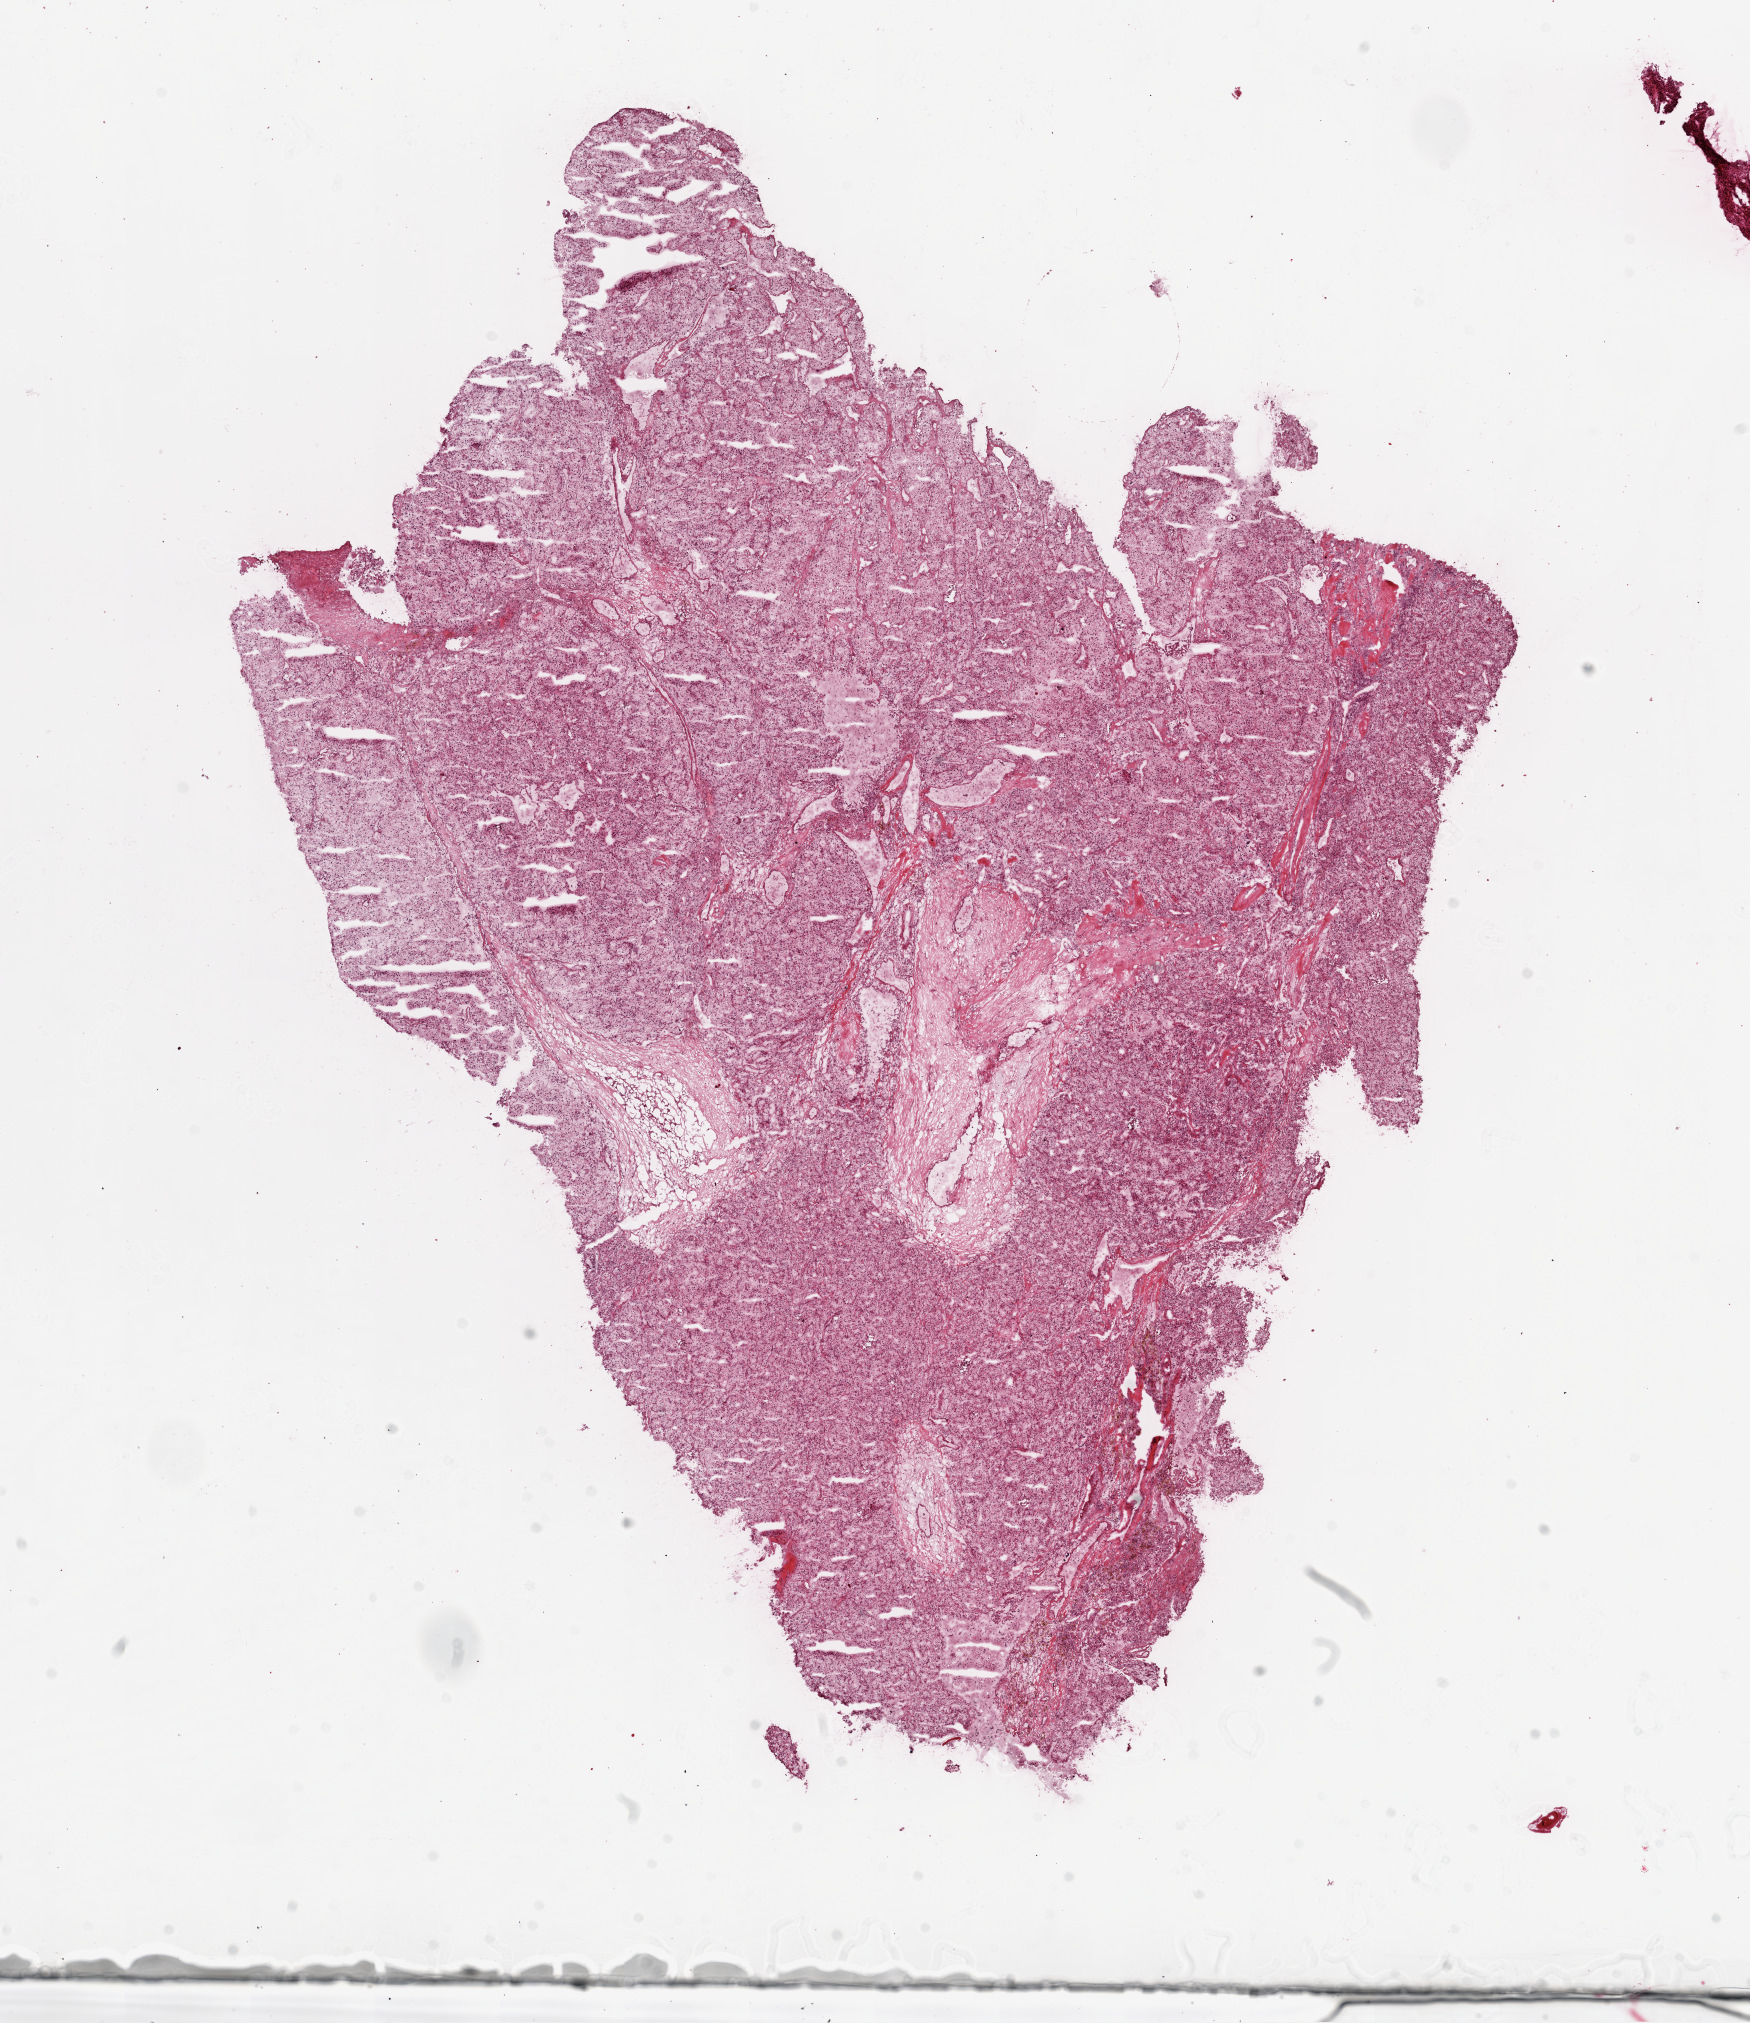
H&E-stained whole-slide image, shown as a low-resolution overview of the whole scanned area (about 14.0 x 16.2 mm), frozen section from the top of the tissue portion, kidney, primary tumour sample. Male, age 79 years at initial diagnosis. Histologic grade: G3 (poorly differentiated). Composition of this section per pathologist review: tumour cells 90%, tumour nuclei 95%, normal cells 0%, stromal cells 10%, necrosis 0%.
Pathologic diagnosis: Clear cell adenocarcinoma, NOS. AJCC pathologic stage: III (6th edition). TNM: T3a NX M0.